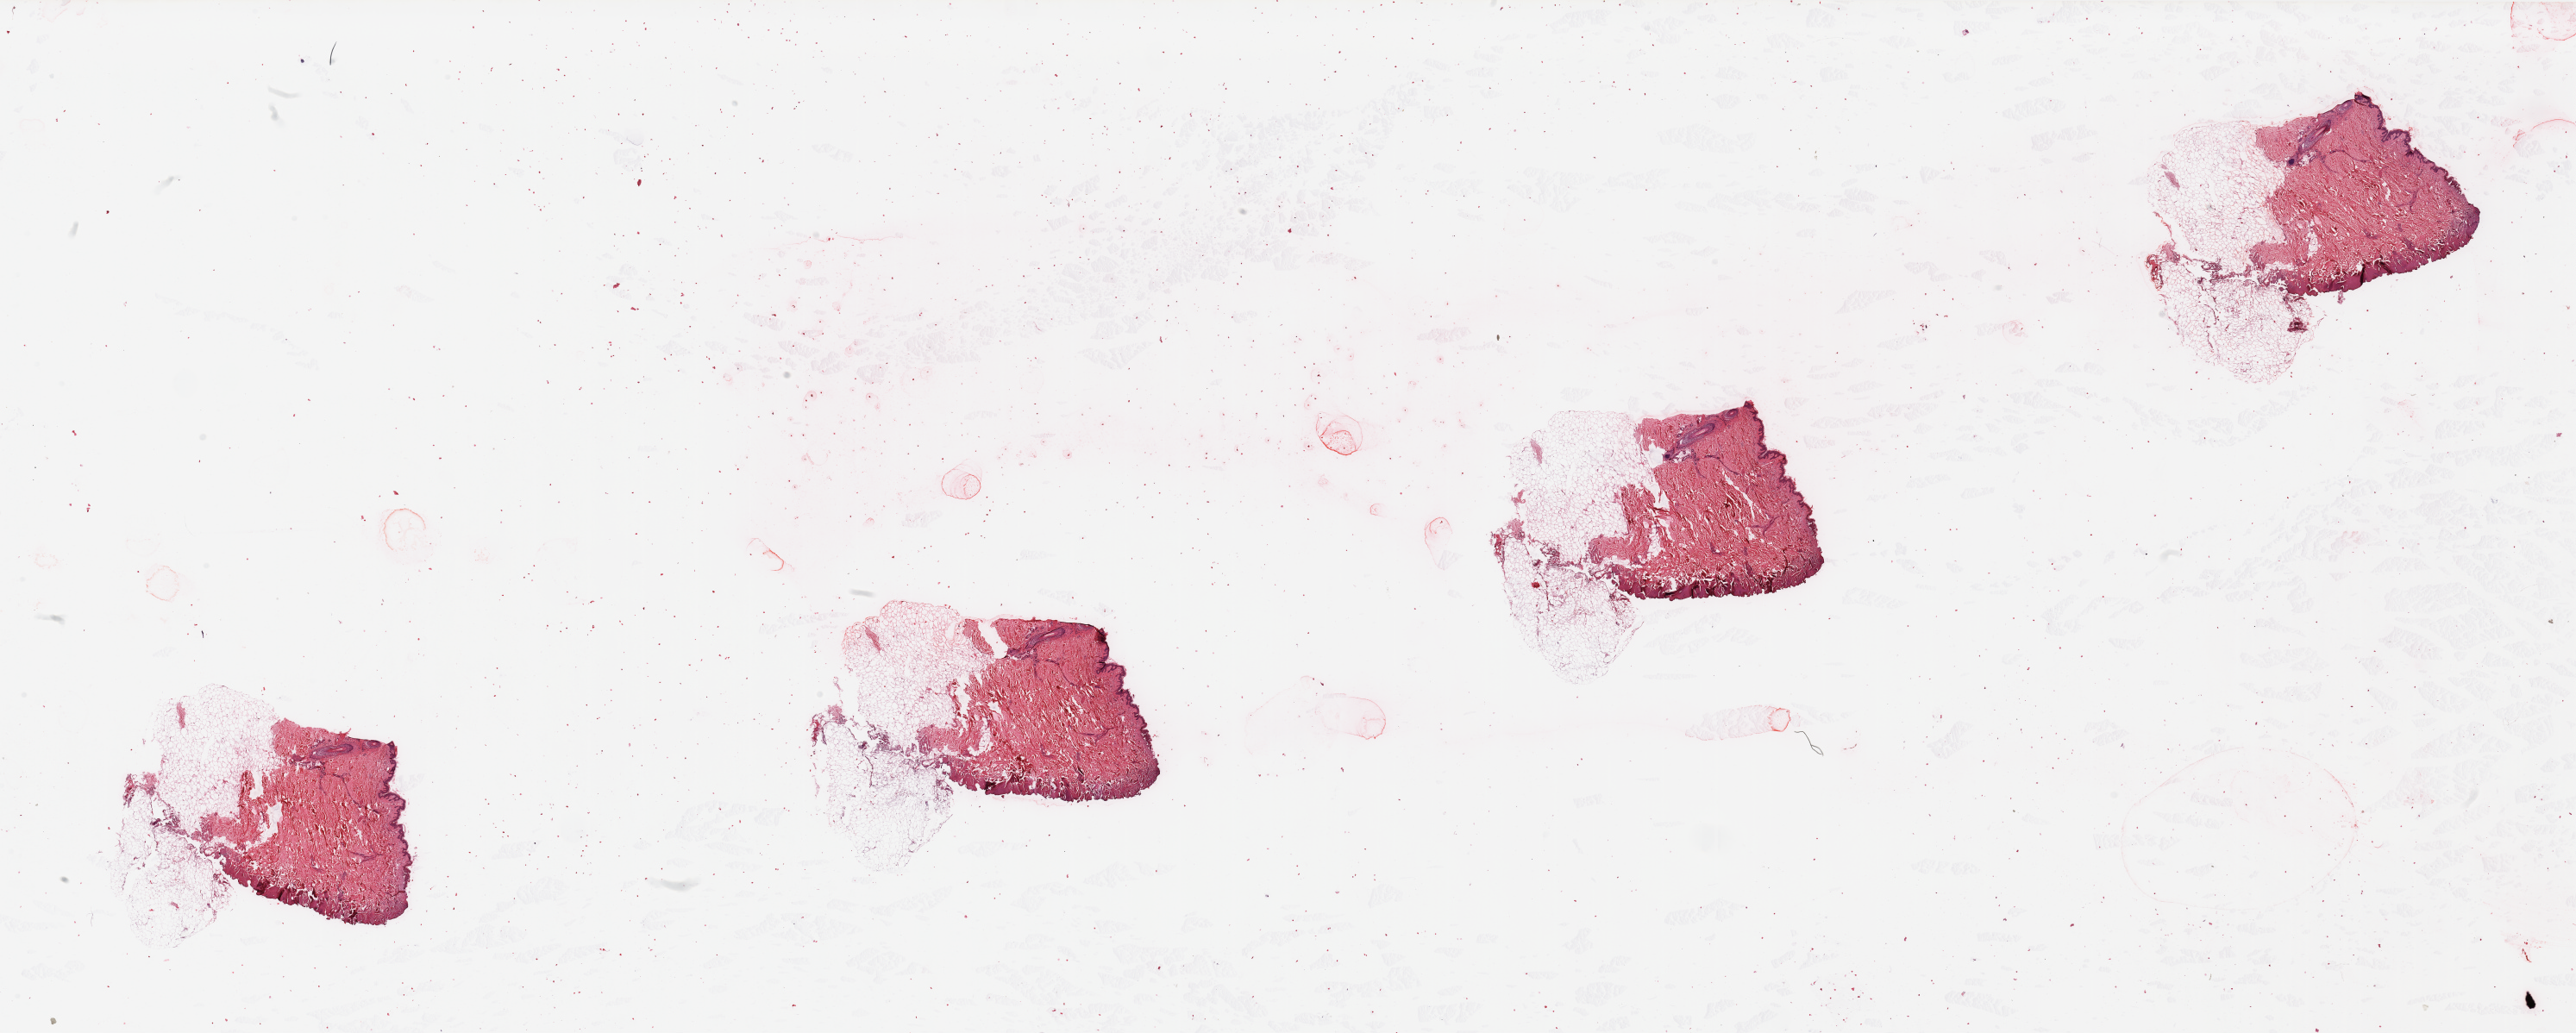
H&E whole-slide image — shown as a low-resolution overview of the whole scanned area (about 47.3 x 19.0 mm, slide scanned at 20x), normal (non-tumour) tissue sample, sampled site: trunk. 69-year-old male patient.
• this section: normal (non-tumour) tissue from the same patient
• patient diagnosis: Malignant melanoma, NOS